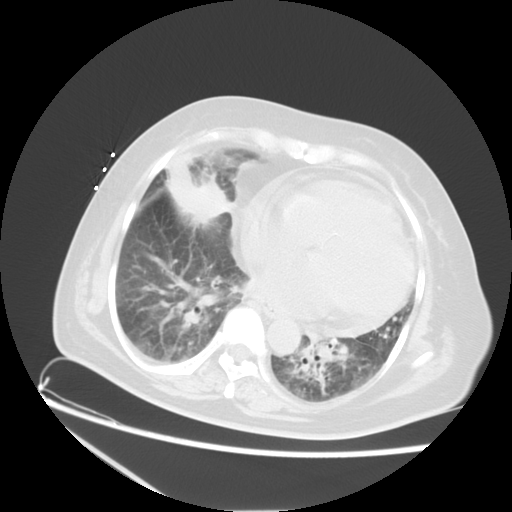
Chest CT, one axial slice. Slice 6 of 22 in the series (ordered by position). Reconstruction kernel STANDARD. Lung window (W 1500 / L -600 HU). 512 × 512 image matrix, field of view 350 × 350 mm. Patient: female, 67 years. From the clinical record (not read from this slice): clinical TNM (as recorded): T2a N3 M1a.
Outlined on this slice (bounding box drawn by a radiologist):
- lung tumour (recorded histology: adenocarcinoma): bounding box (x1, y1, x2, y2) in pixels: (165, 169, 229, 227)